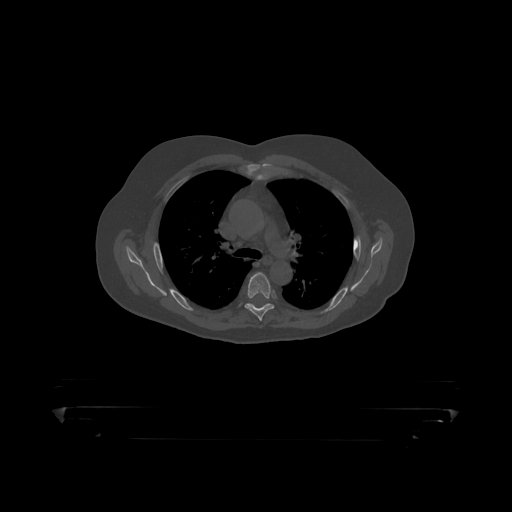
CT including the spine, one axial slice. Position 319 of 390 along the scan axis. Reconstruction kernel STANDARD. 120 kVp. Bone window (W 1800 / L 400 HU). 1.25 mm slice thickness. 512 × 512 image matrix, field of view 650 × 650 mm. Patient: male, 60 years. Case-level facts recorded for this patient, not image findings: primary cancer: prostate.
Annotated regions visible in this slice (semi-automatically segmented with operator editing):
- T5 vertebra: bounding box (x1, y1, x2, y2) in pixels: (245, 273, 274, 319)
- T6 vertebra: (248, 304, 274, 308)